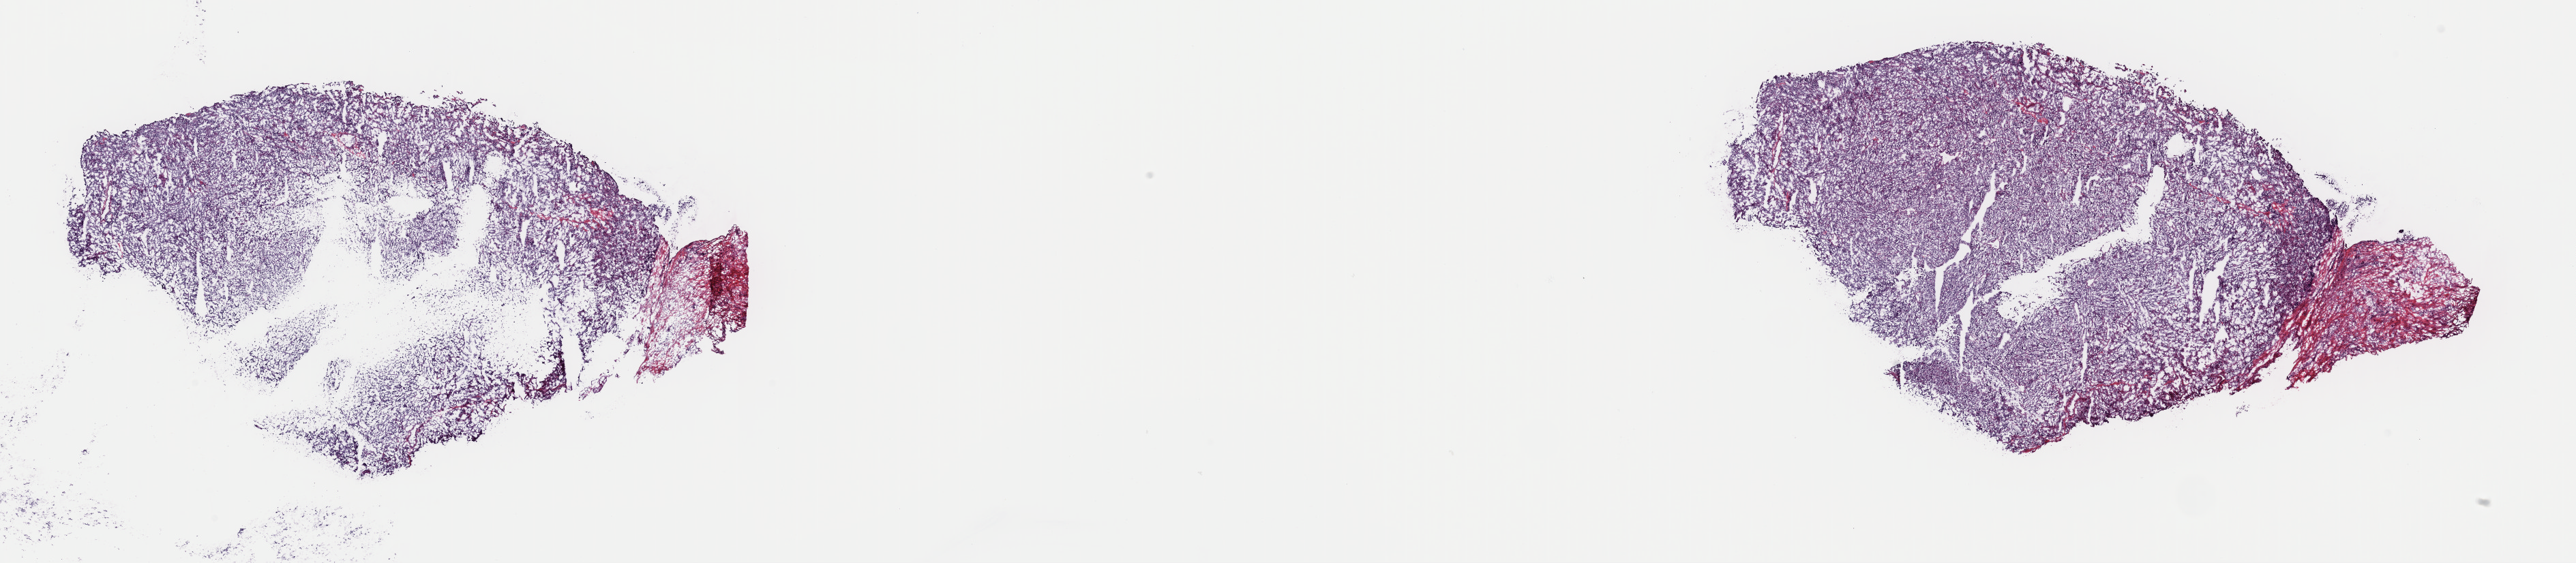
H&E-stained whole-slide image, low-resolution overview of the scanned area, about 29.8 x 6.5 mm, frozen section from the top of the tissue portion, spinal cord, cranial nerves, and other parts of central nervous system, additional new primary tumour sample. Patient: male, age at initial diagnosis 55 years. Slide review estimates, as recorded: tumour cells 100%, tumour nuclei 75%, normal cells 0%, stromal cells 0%, necrosis 0%. Infiltration values recorded for this section: lymphocyte infiltration 2%, monocyte infiltration 0%, neutrophil infiltration 0%.
This section: additional new primary tumour. Patient diagnosis: Paraganglioma, malignant (nervous system, NOS).